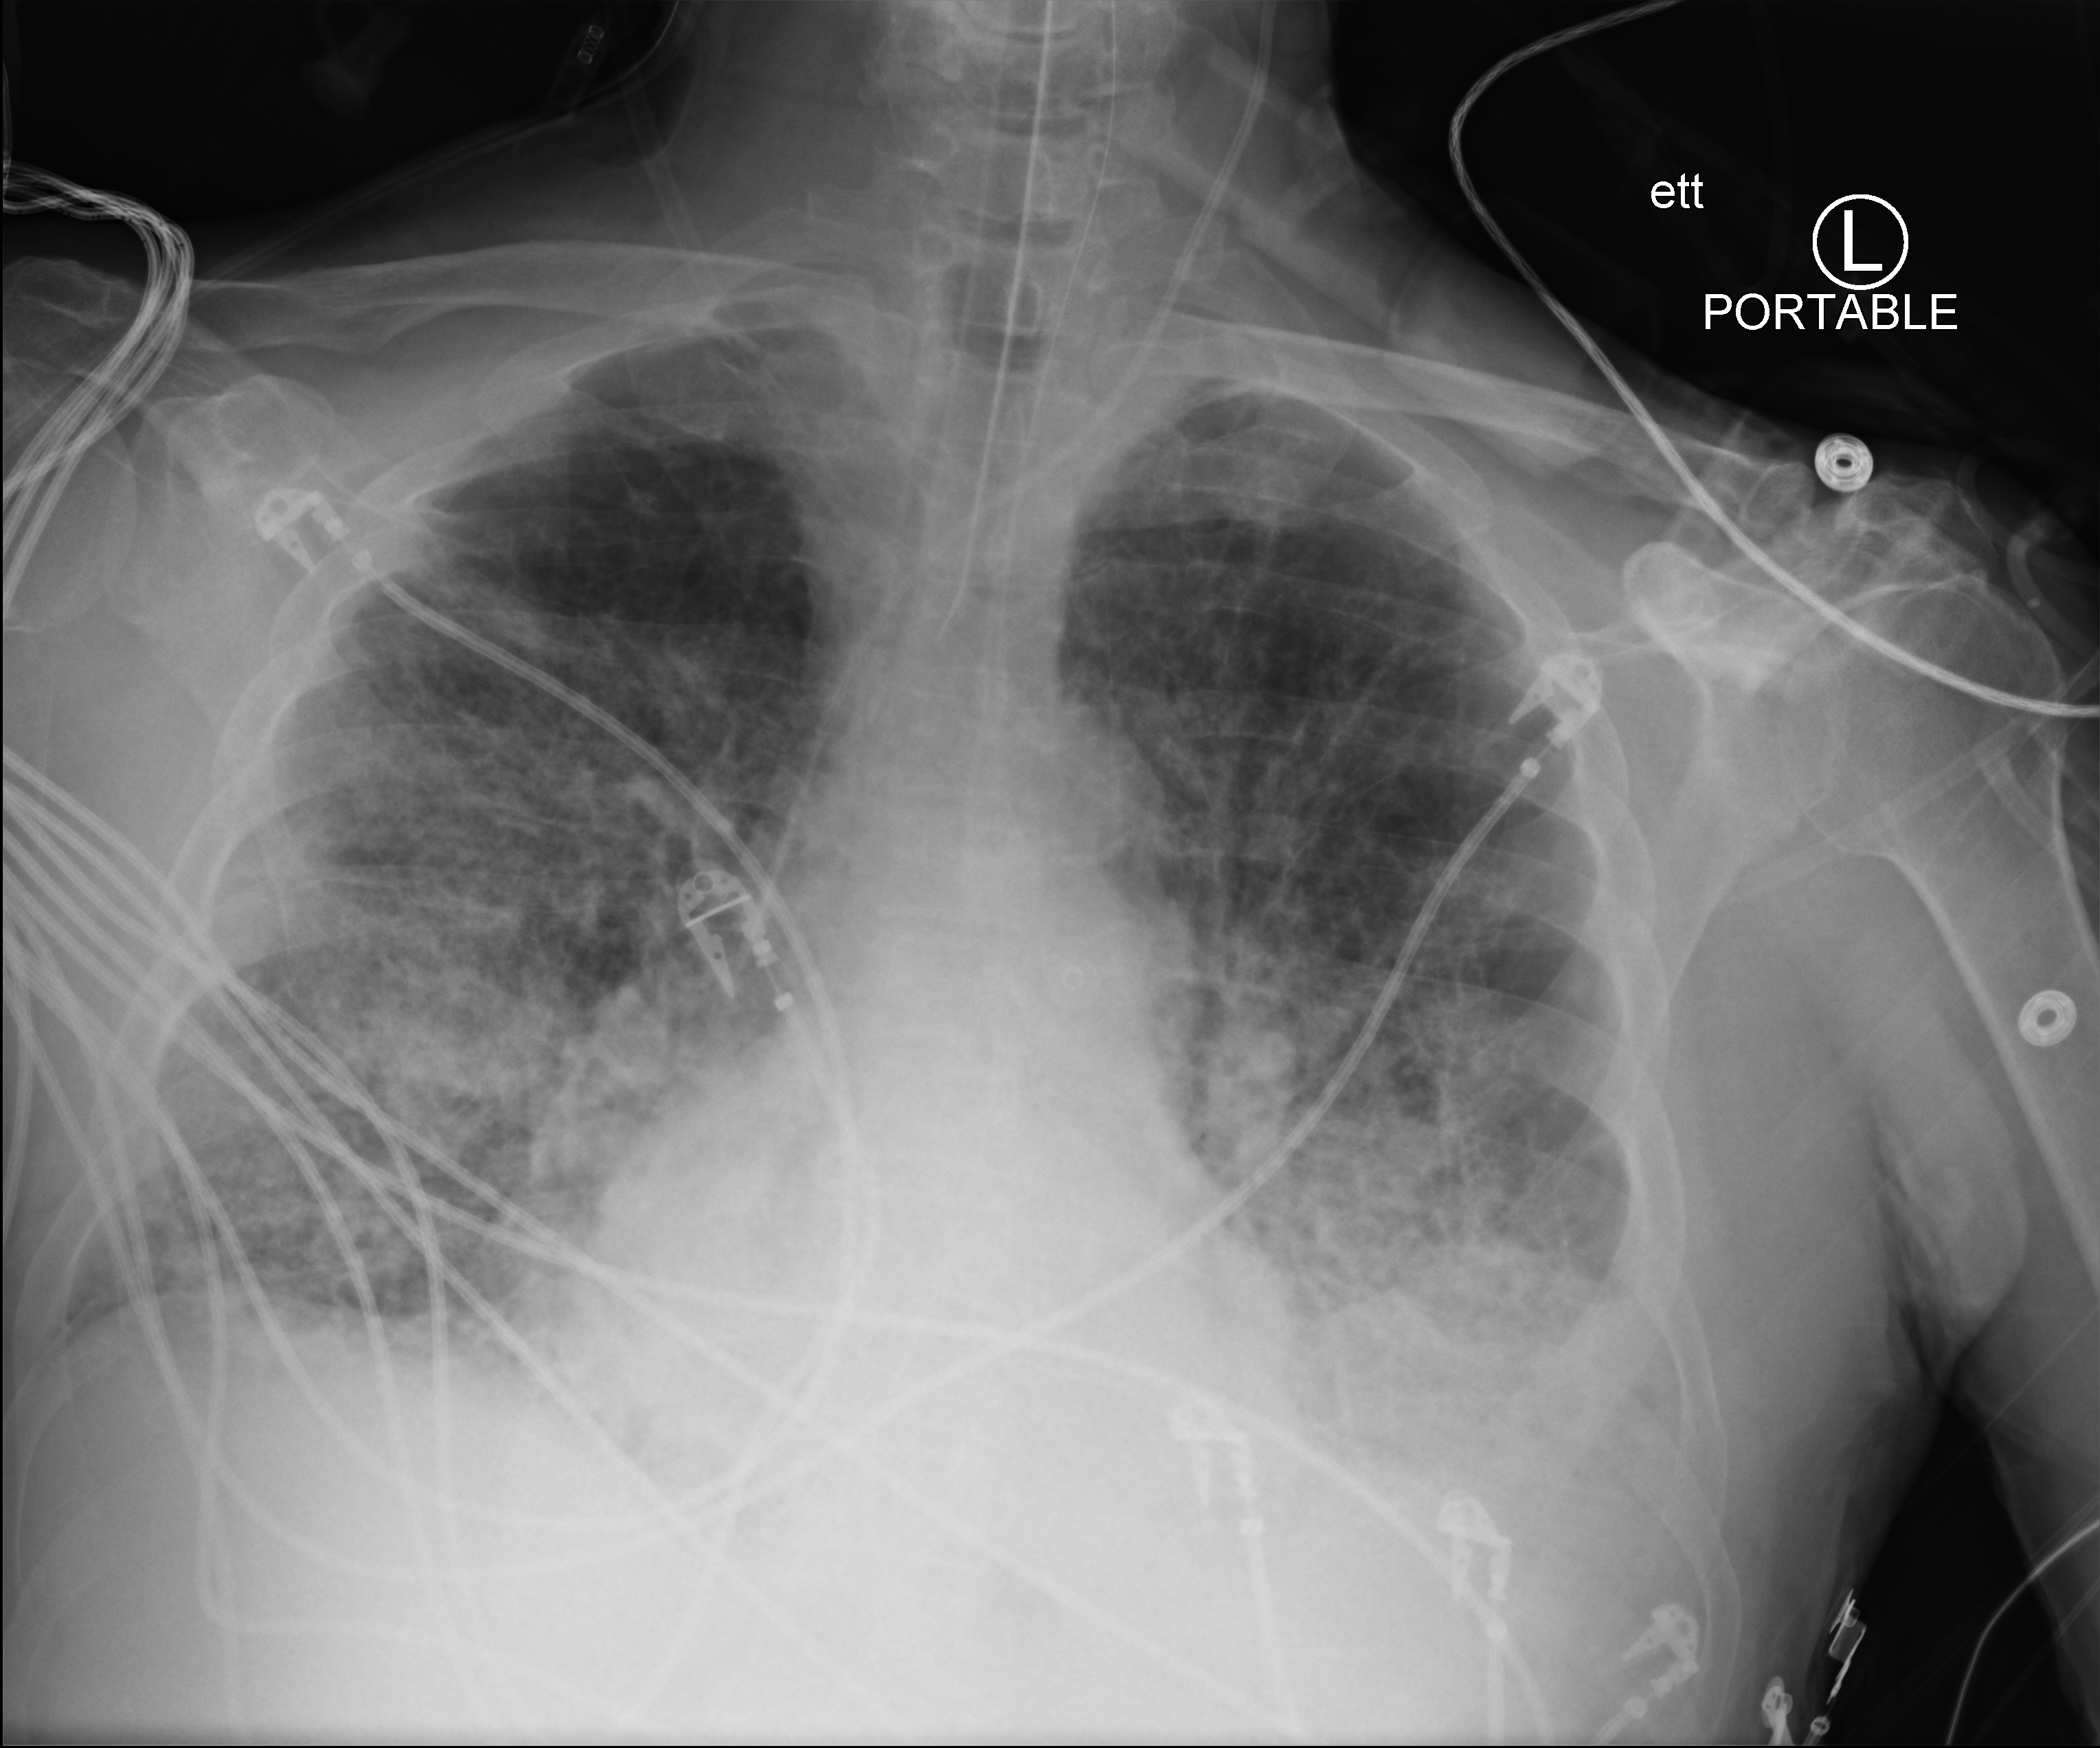
Chest X-ray (portable), anteroposterior (AP) projection. Patient hospitalised with COVID-19; male, aged 75–90 years.
Hospital-stay facts (about this admission, not read from this image; timing relative to this image not recorded):
- diabetes (admission record): no